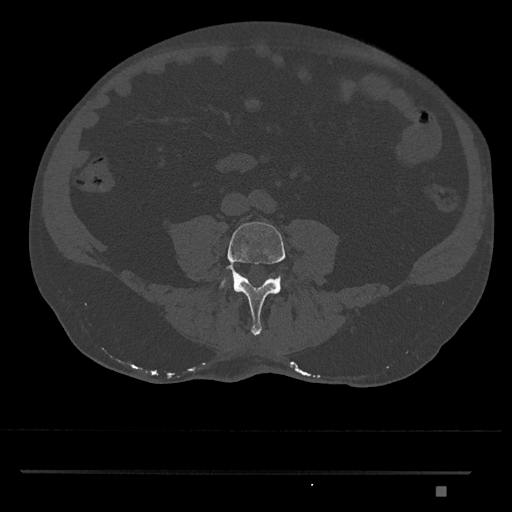
CT including the spine, one axial slice. Position 610 of 1134 along the scan axis. Bone window (W 1800 / L 400 HU). 0.5 mm slice thickness. 512 × 512 image matrix, field of view 429 × 429 mm. Patient: male, 65 years. From the clinical record (not read from this slice): primary cancer: prostate.
Annotated regions visible in this slice (semi-automatic segmentation, software-assisted and operator-edited):
- L4 vertebra: bounding box (x1, y1, x2, y2) in pixels: (219, 221, 286, 335)